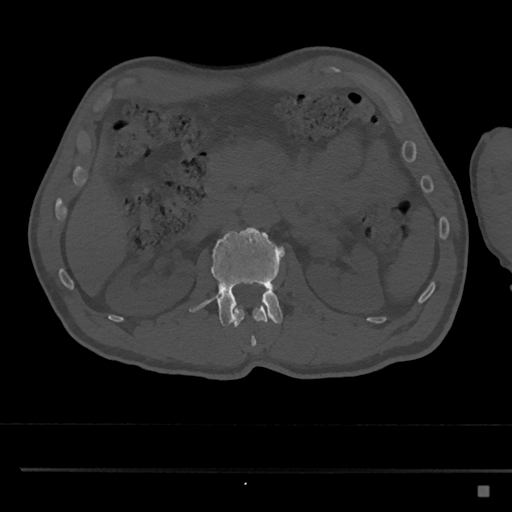
CT including the spine, one axial slice; position 784 of 797 along the scan axis; reconstruction kernel Br40s/3; bone window (W 1800 / L 400 HU); 512 × 512 image matrix, field of view 391 × 391 mm. Male patient, age 59 years. Case-level facts recorded for this patient, not image findings: primary cancer: prostate.
Annotated regions visible in this slice (semi-automatic segmentation, software-assisted and operator-edited):
- L1 vertebra: bounding box (x1, y1, x2, y2) in pixels: (233, 303, 269, 346)
- L2 vertebra: (188, 227, 285, 327)